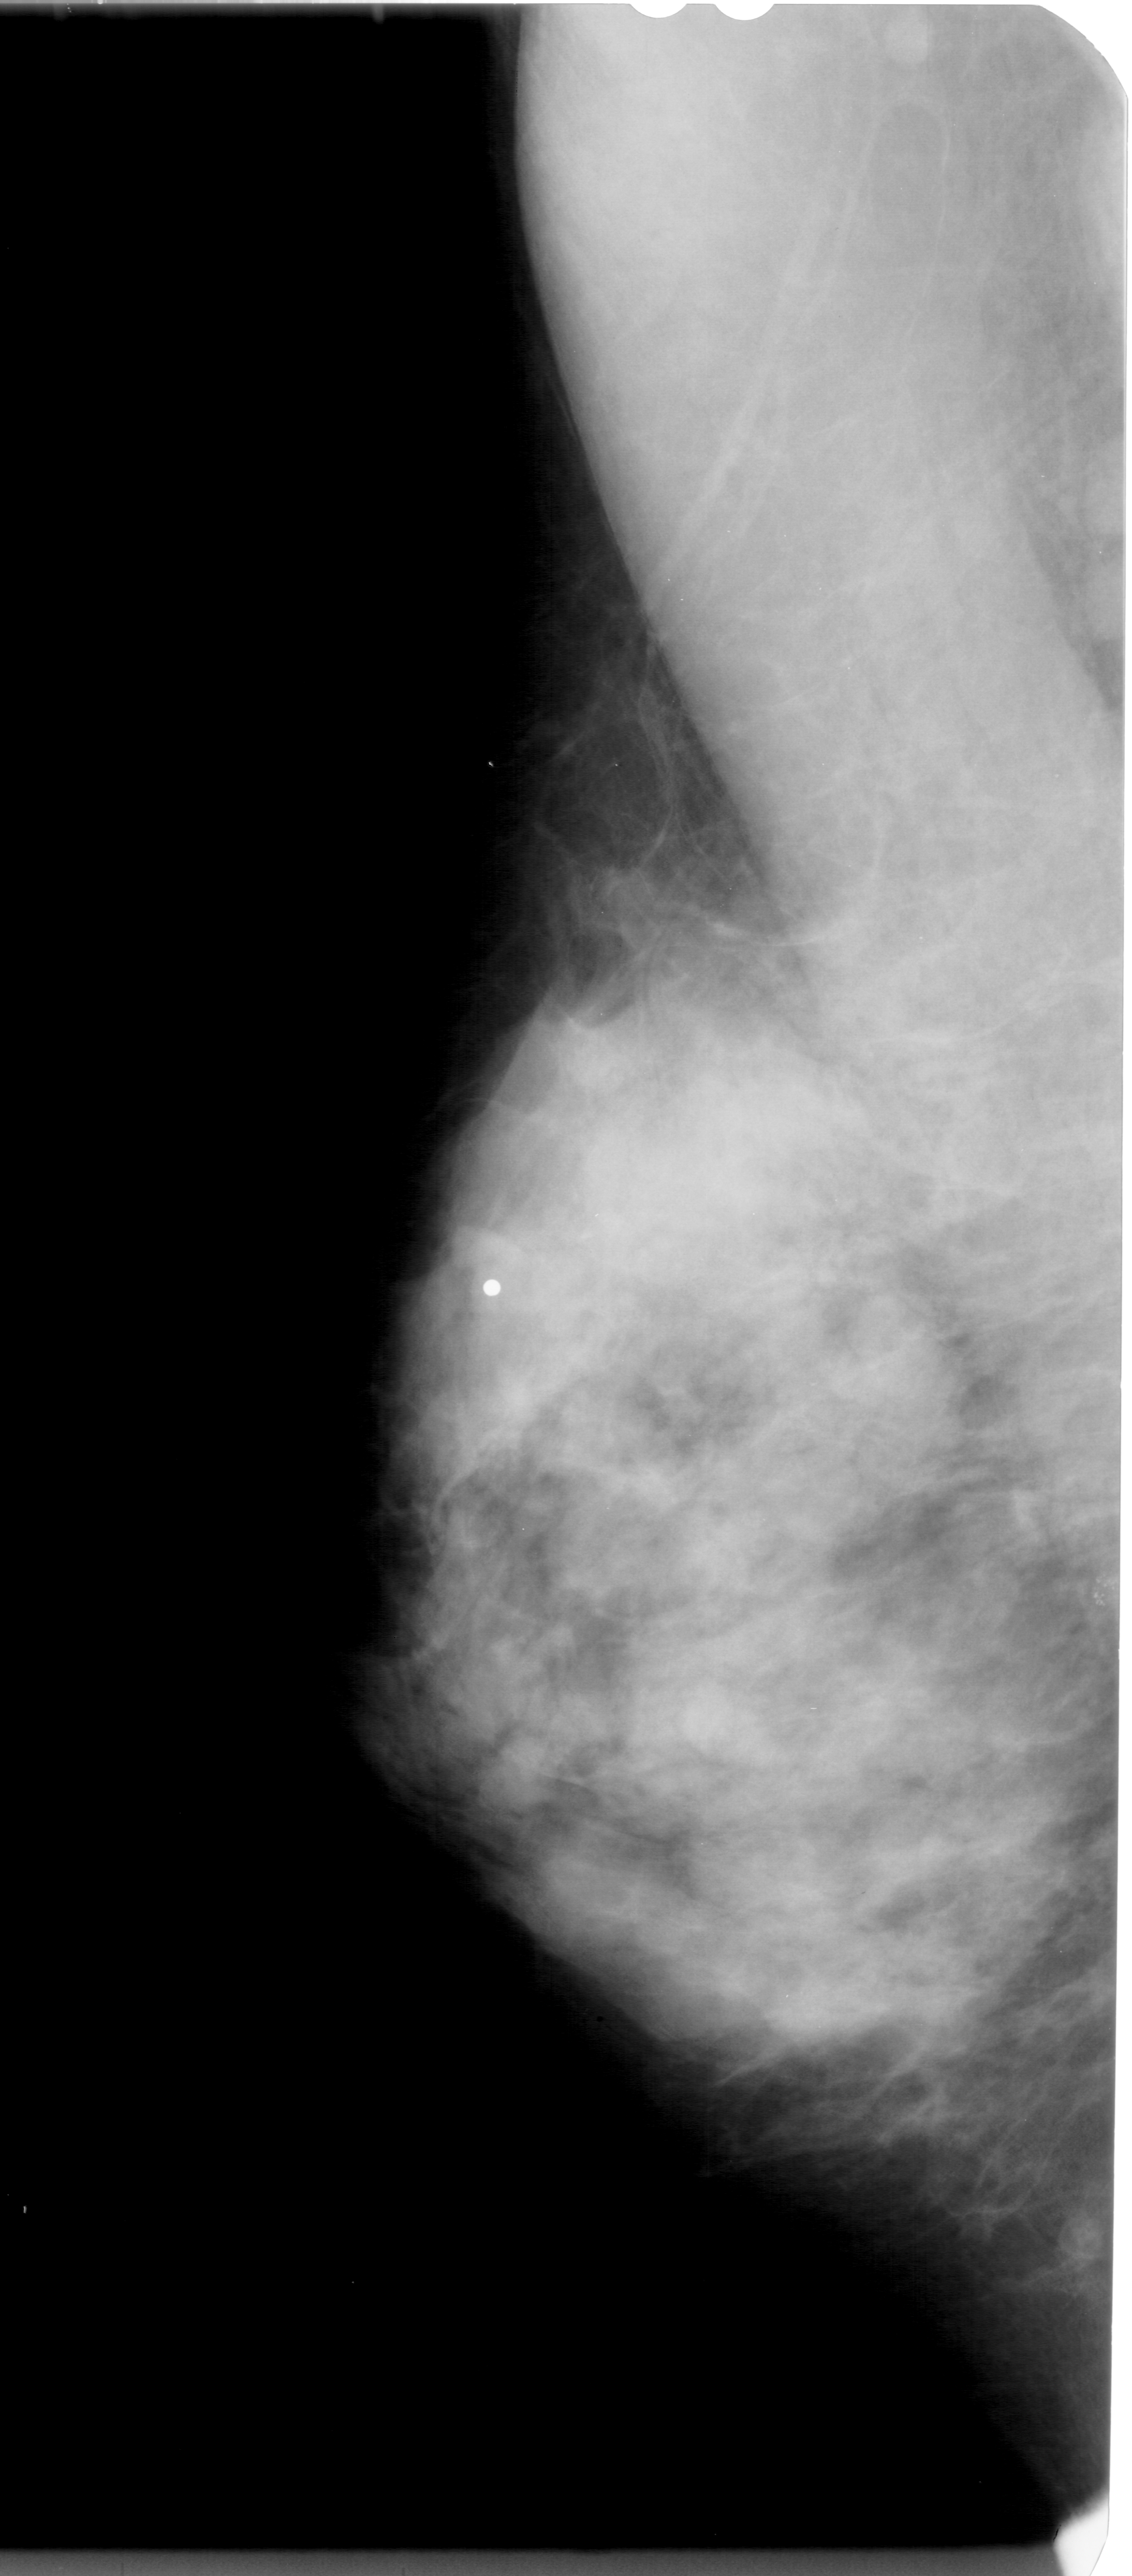
Digitized screen-film mammogram. Left breast. MLO view. 1132 × 2576 image matrix.
Marked abnormalities (boxes around the expert regions of interest):
- calcifications, morphology pleomorphic, distribution clustered; BI-RADS assessment category 4; subtlety rating 2 on a 1 (subtle) to 5 (obvious) scale; pathology (as recorded): benign: bounding box [x1, y1, x2, y2] px = [1092, 1572, 1128, 1624]